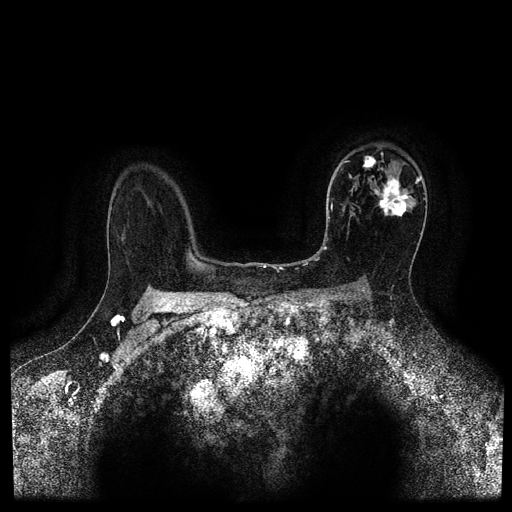
Breast MRI (dynamic contrast-enhanced, multi-phase), one axial slice; dynamic contrast-enhanced series, time point 2 of 5 at this slice position (early post-contrast); 1.5 T; TE 2.7 ms, TR 5.4 ms; 2 mm slice thickness; 512 × 512 image matrix, field of view 340 × 340 mm. Female patient, age 50 years.
Outlined on this slice (semi-automatic segmentation, software-assisted and operator-edited):
- breast lesion (labelled 'tumour' in the annotation; benign lesions carry a separate 'benign' label): bounding box <371,175,413,219> (left, top, right, bottom; pixels)
- breast lesion (labelled 'tumour' in the annotation; benign lesions carry a separate 'benign' label): <362,155,381,170>